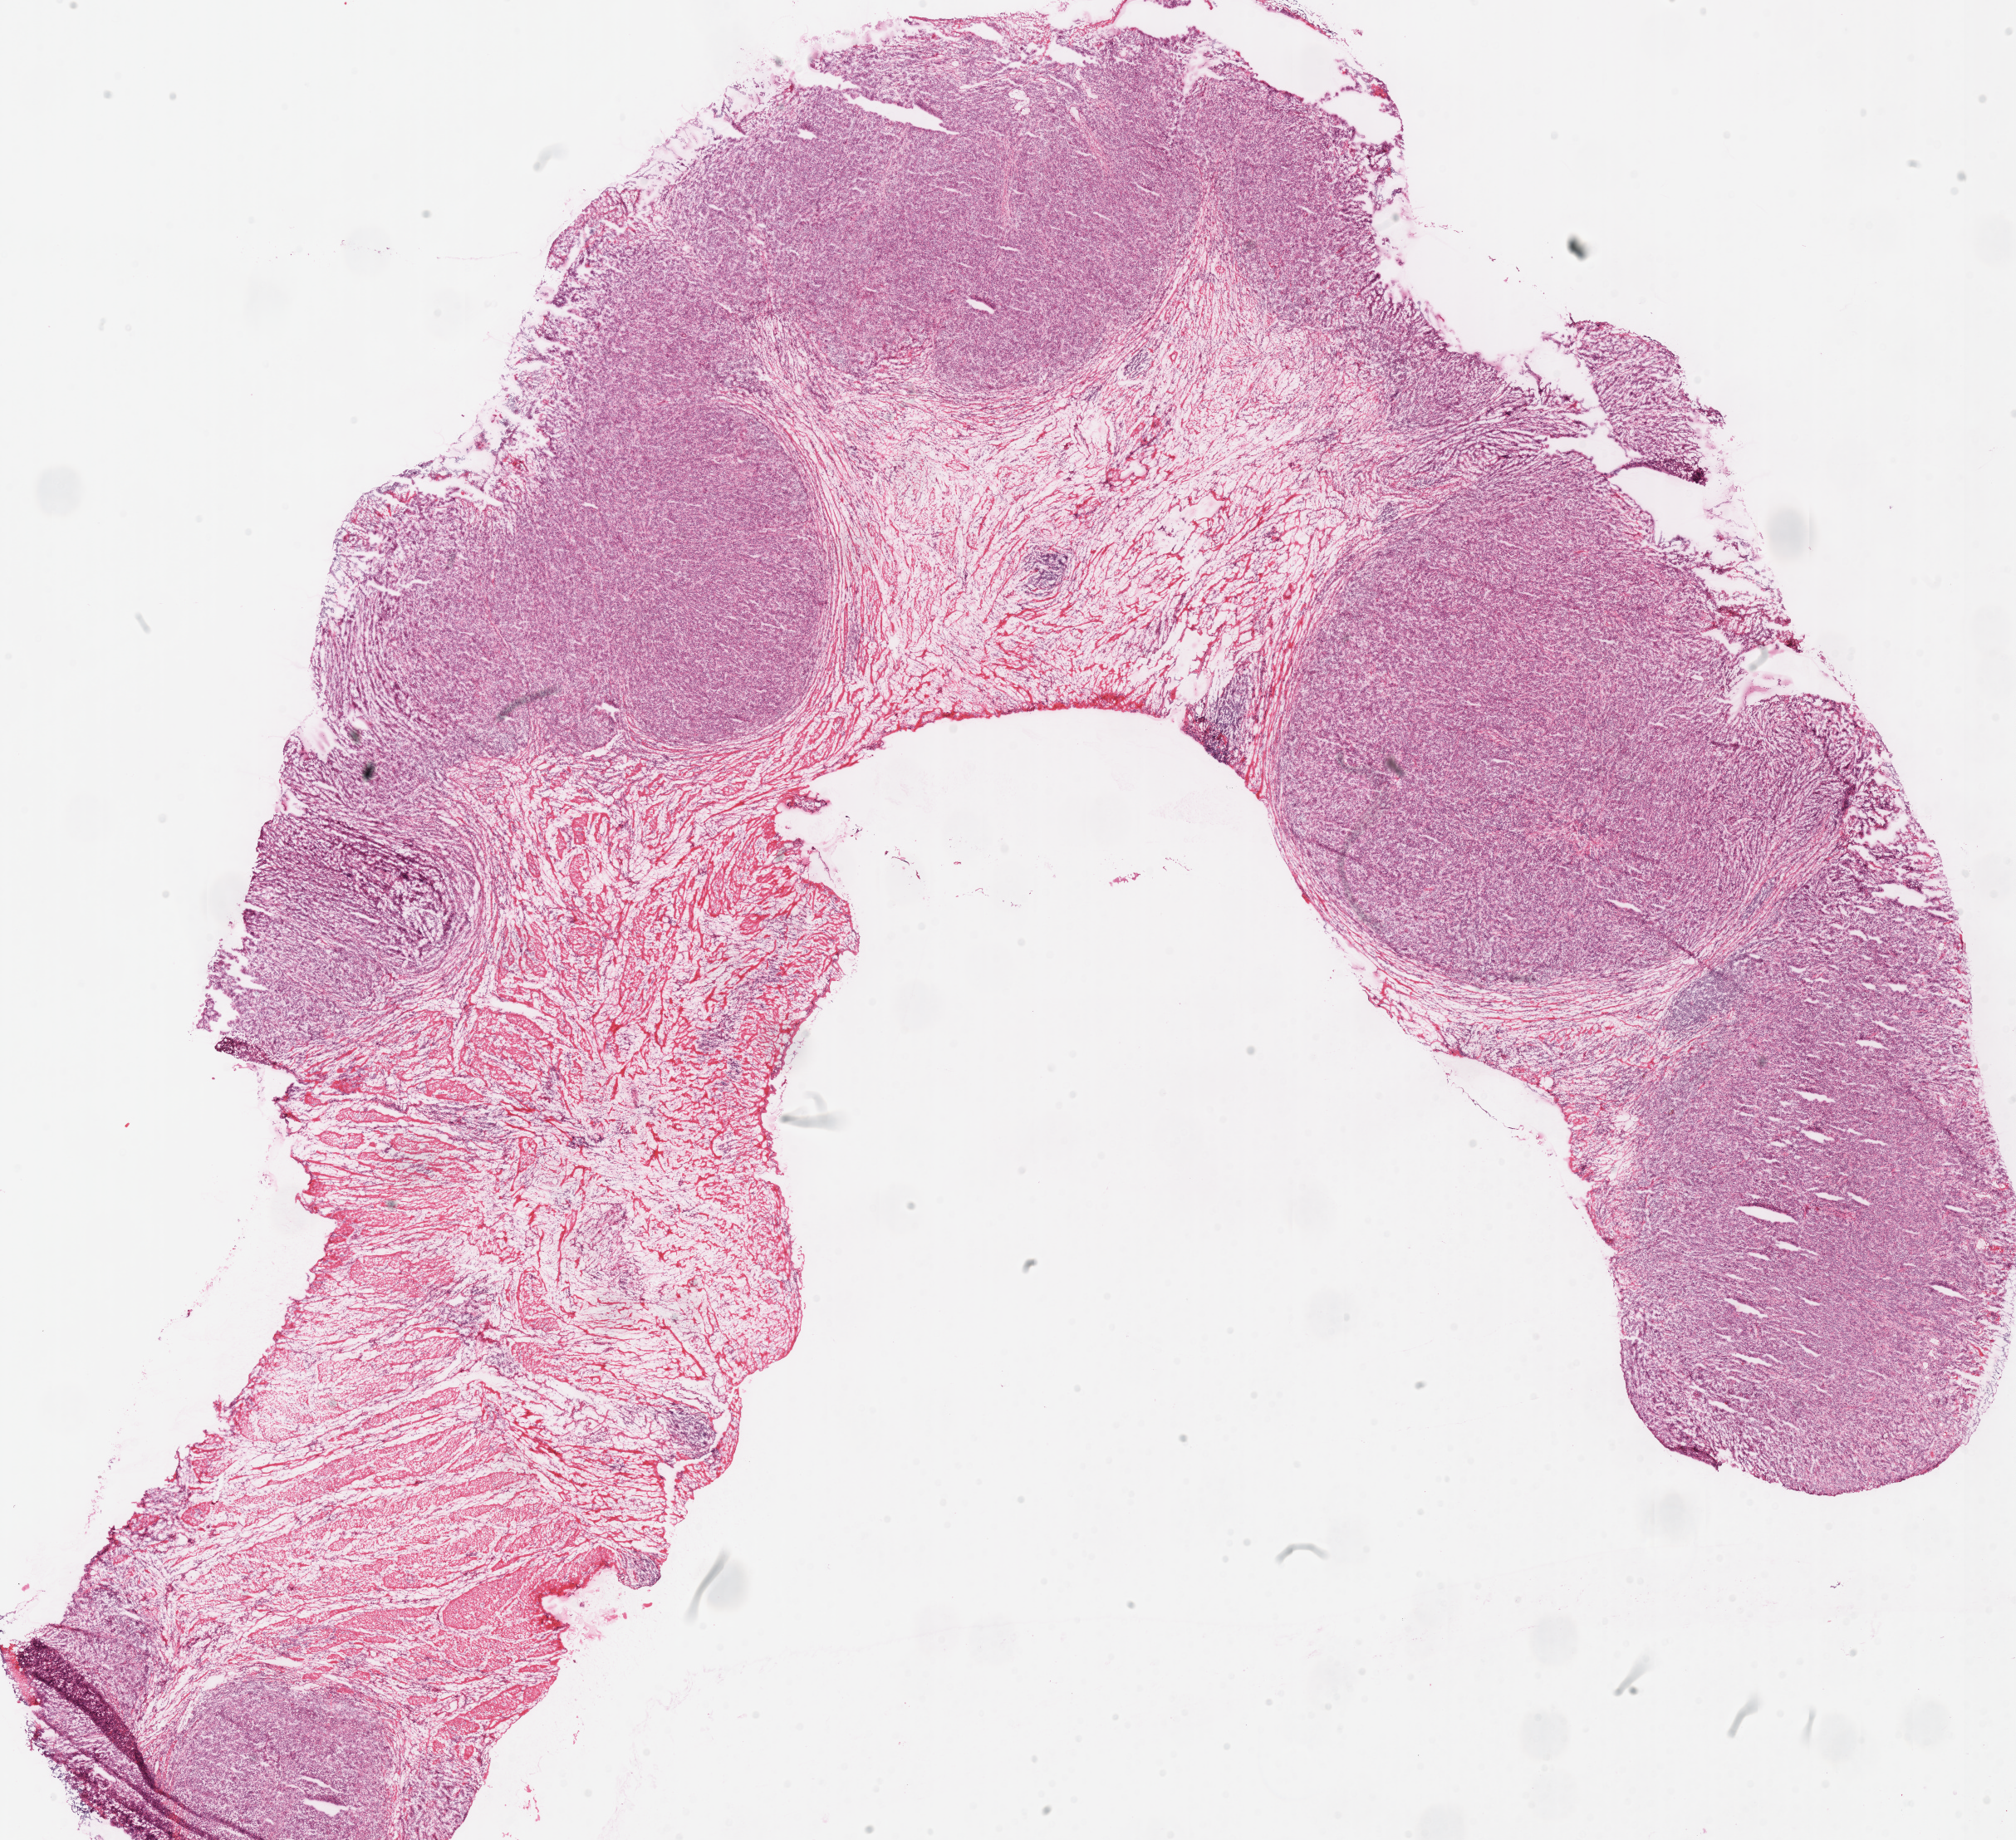
Whole-slide histology image, H&E, whole scanned area (about 19.1 x 17.4 mm) shown as a low-resolution overview. Frozen section from the top of the tissue portion. Sample: primary tumour, stomach. Female patient; age at initial diagnosis 73 years. Histologic grade: G3 (poorly differentiated). Pathologist review of this section (percent, as recorded): tumour cells 50%, tumour nuclei 60%, normal cells 0%, stromal cells 50%, necrosis 0%.
* AJCC pathologic stage: IB (7th edition)
* lymph nodes positive (case pathology): 0 of 11 examined
* TNM: T2 N0 M0
* histologic diagnosis: Adenocarcinoma, NOS (fundus of stomach)